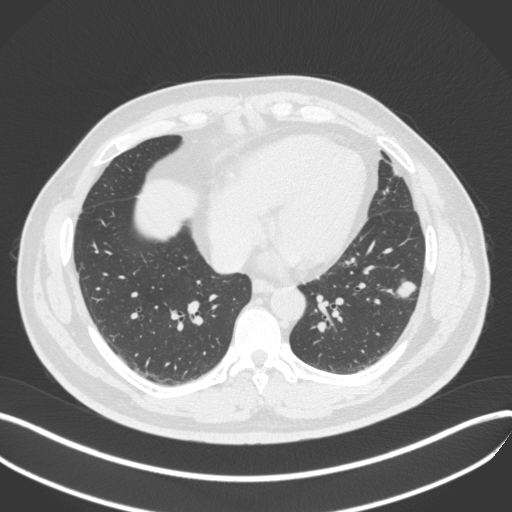
Chest CT, one axial slice; slice 152 of 420 in the series (ordered by position); 120 kVp; lung window (W 1500 / L -600 HU); 1 mm slice thickness; 512 × 512 image matrix, field of view 400 × 400 mm. Male patient, age 39 years. Case-level facts recorded for this patient, not image findings: clinical TNM (as recorded): T2a N0 M0; histopathological grade: G2-3.
Outlined on this slice (bounding box drawn by a radiologist):
- lung tumour (recorded histology: adenocarcinoma): box from (x=392, y=275) to (x=420, y=303) px